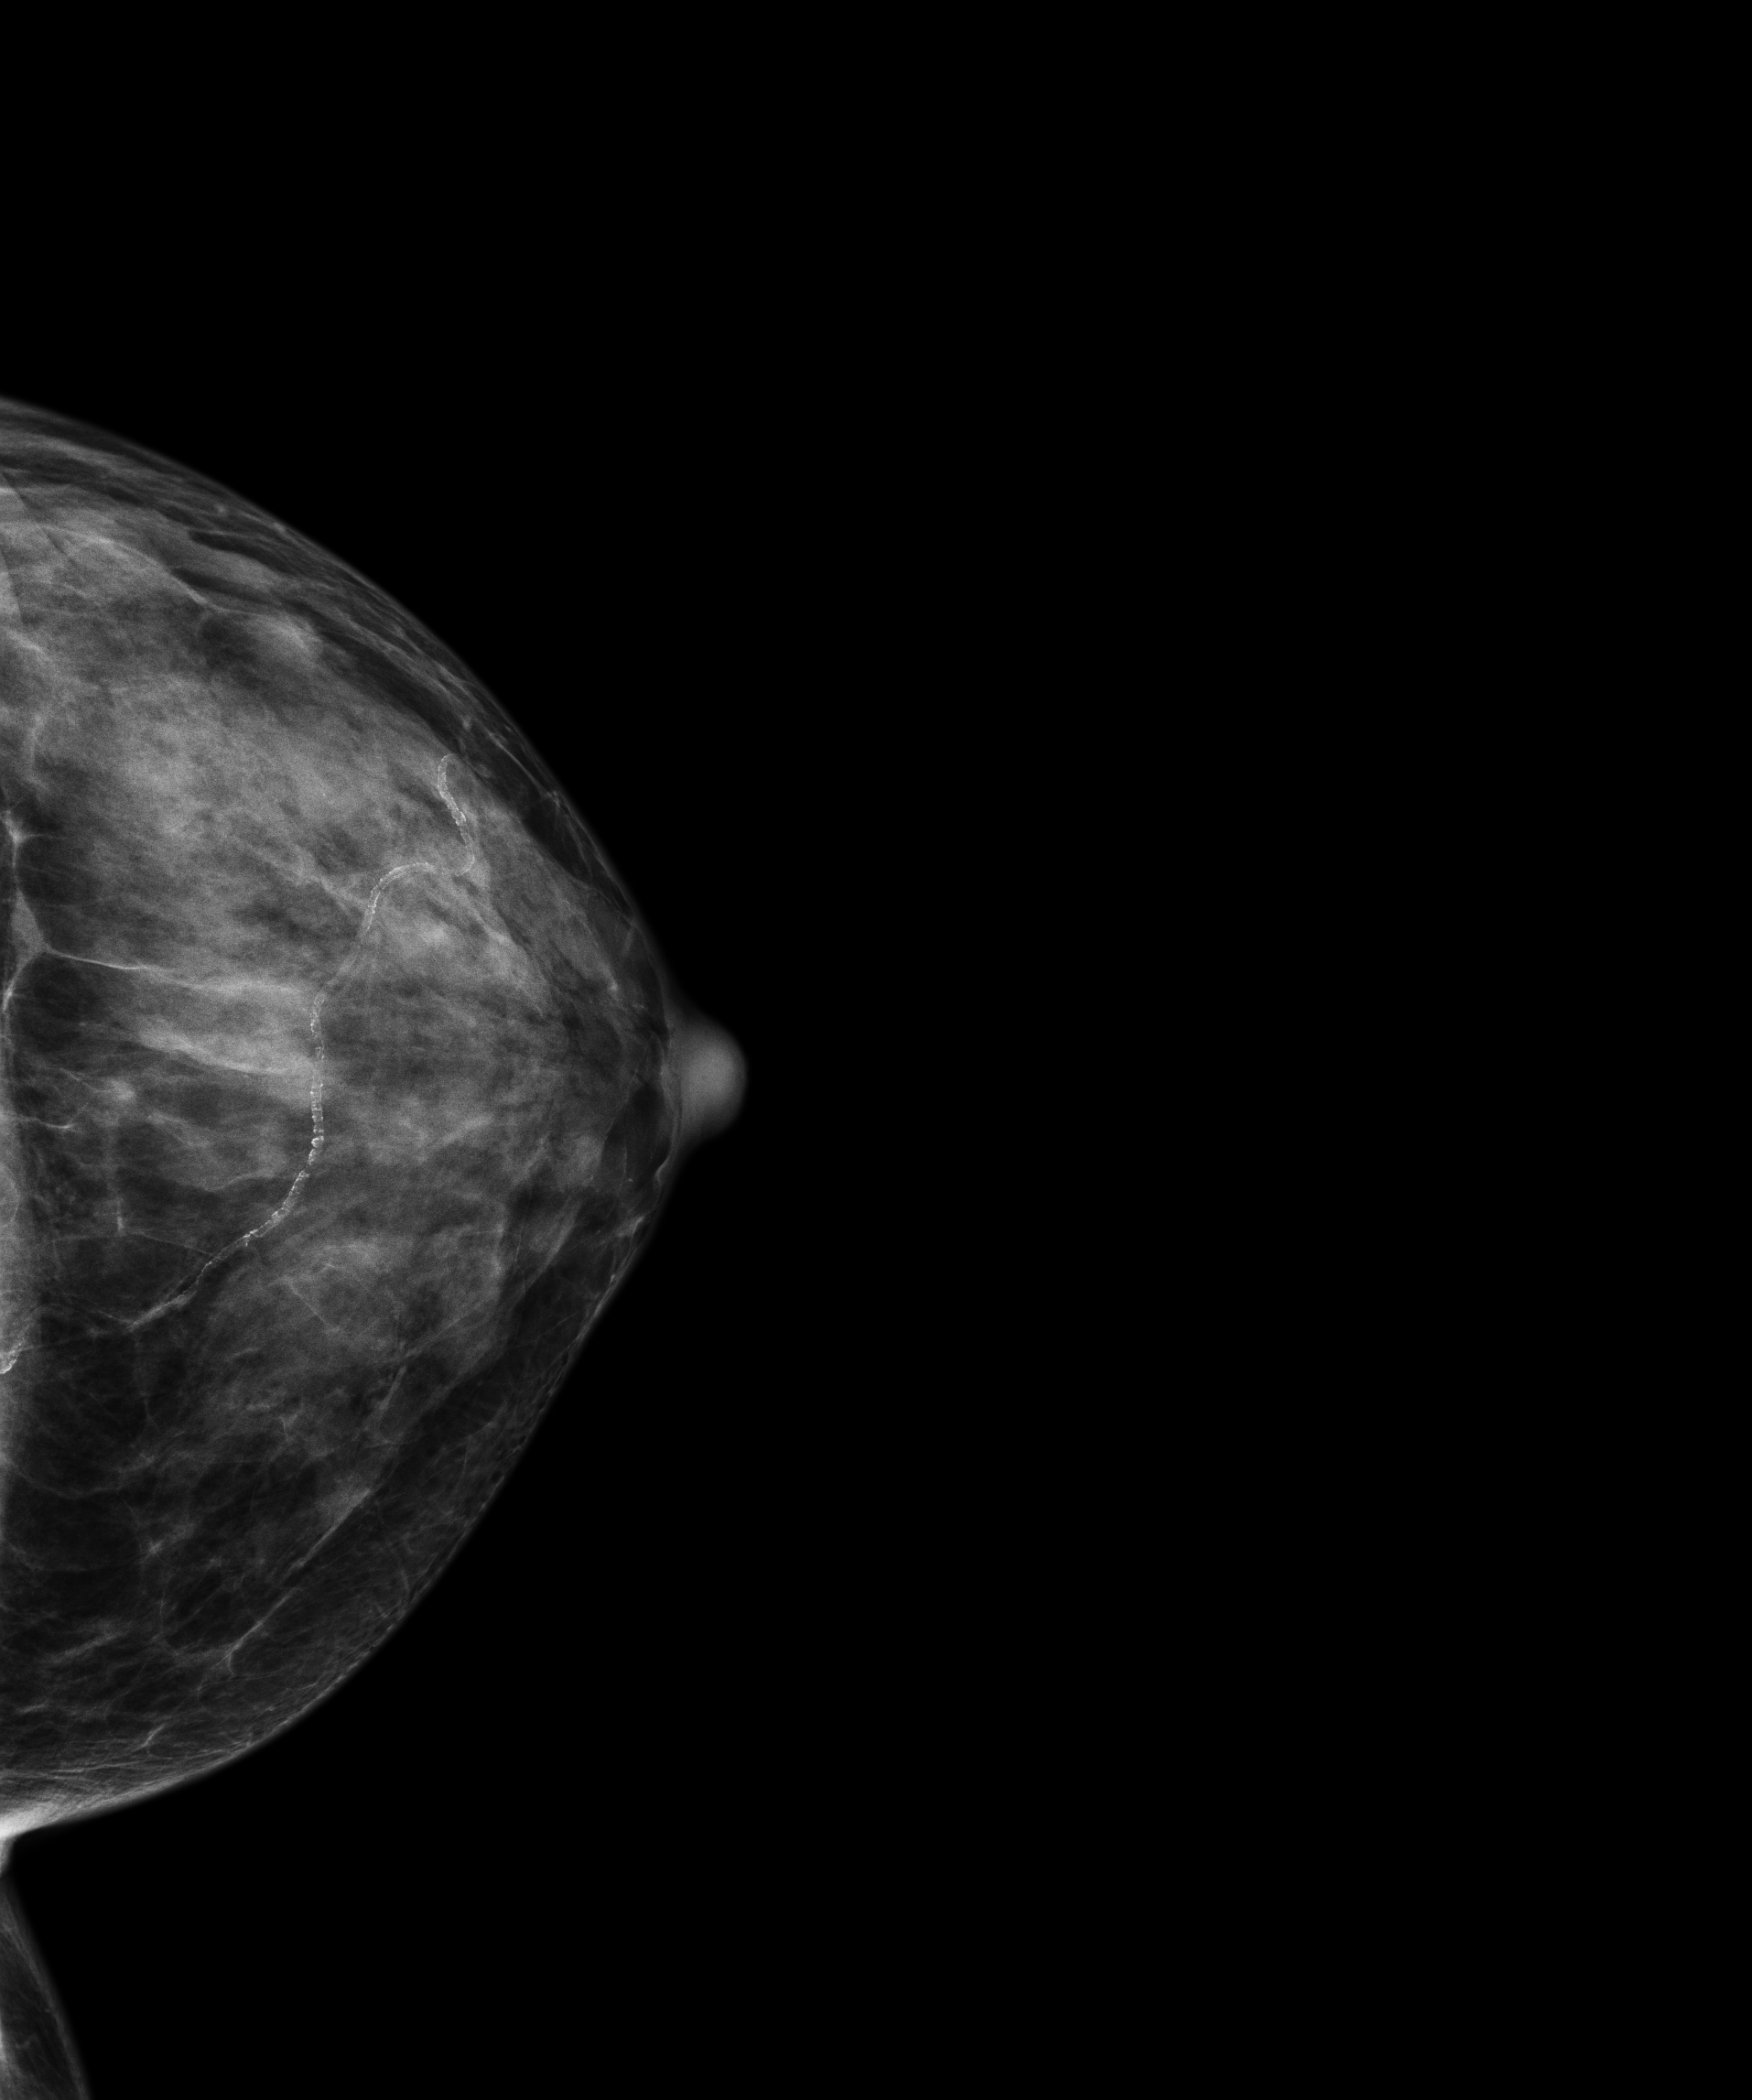
Screening examination. Patient: female, 60 years.
Image type: full-field digital mammogram. Breast: left. Projection: cranio-caudal projection.